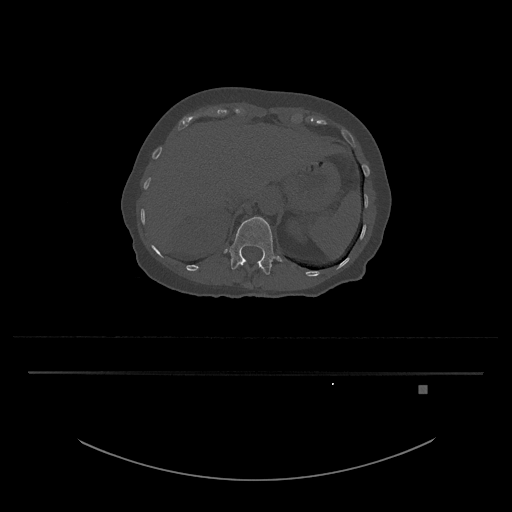
CT including the spine, one axial slice. Slice 568 of 797 in the series (ordered by position). Reconstruction kernel Br40s/3. 120 kVp. Bone window (W 1800 / L 400 HU). 512 × 512 image matrix, field of view 500 × 500 mm. Patient: female, 57 years. From the clinical record (not read from this slice): primary cancer: cervical.
Annotated regions visible in this slice (semi-automatic segmentation, software-assisted and operator-edited):
- L1 vertebra: bounding box (x1, y1, x2, y2) in pixels: (223, 217, 284, 275)
- T12 vertebra: (242, 262, 263, 270)